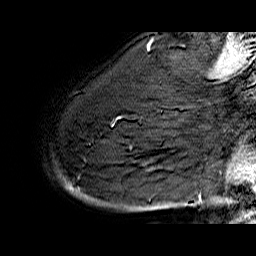
Breast MRI (dynamic contrast-enhanced), one sagittal slice. Position 49 of 60 along the scan axis. Dynamic contrast-enhanced series, time point 2 of 6 at this slice position (early post-contrast). 1.5 T. TE 6.4 ms, TR 32.9 ms. 256 × 256 image matrix, field of view 200 × 200 mm. Female patient. From the clinical record (not read from this slice): setting: breast cancer imaged before/during neoadjuvant chemotherapy; receptor status: HR-positive, HER2-negative.
Annotated regions visible in this slice (semi-automatic segmentation, software-assisted and operator-edited):
- analysis volume of interest (the breast-tissue region the enhancement analysis was run in; not a lesion): box from (x=58, y=74) to (x=176, y=210) px
- tumour enhancement mask (voxels above the 100 % enhancement threshold inside the analysis volume of interest): (x=66, y=185)–(x=72, y=190)